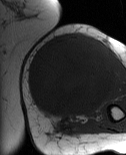
MRI of an extremity soft-tissue mass, one axial slice; position 31 of 86 along the scan axis; MR volume resampled by the dataset authors to the PET/CT grid (not the native acquisition matrix); 3.27 mm slice thickness; 126 × 155 image matrix. Female patient. From the clinical record (not read from this slice): histological type: pleiomorphic leiomyosarcoma; grade: high; site of the primary tumour: left biceps.
Annotated regions visible in this slice (expert contour drawn on MRI and transferred to this co-registered scan by the dataset authors):
- gross tumour volume including surrounding oedema: box from (x=27, y=35) to (x=117, y=121) px
- gross tumour volume (mass): (x=27, y=35)–(x=117, y=118)